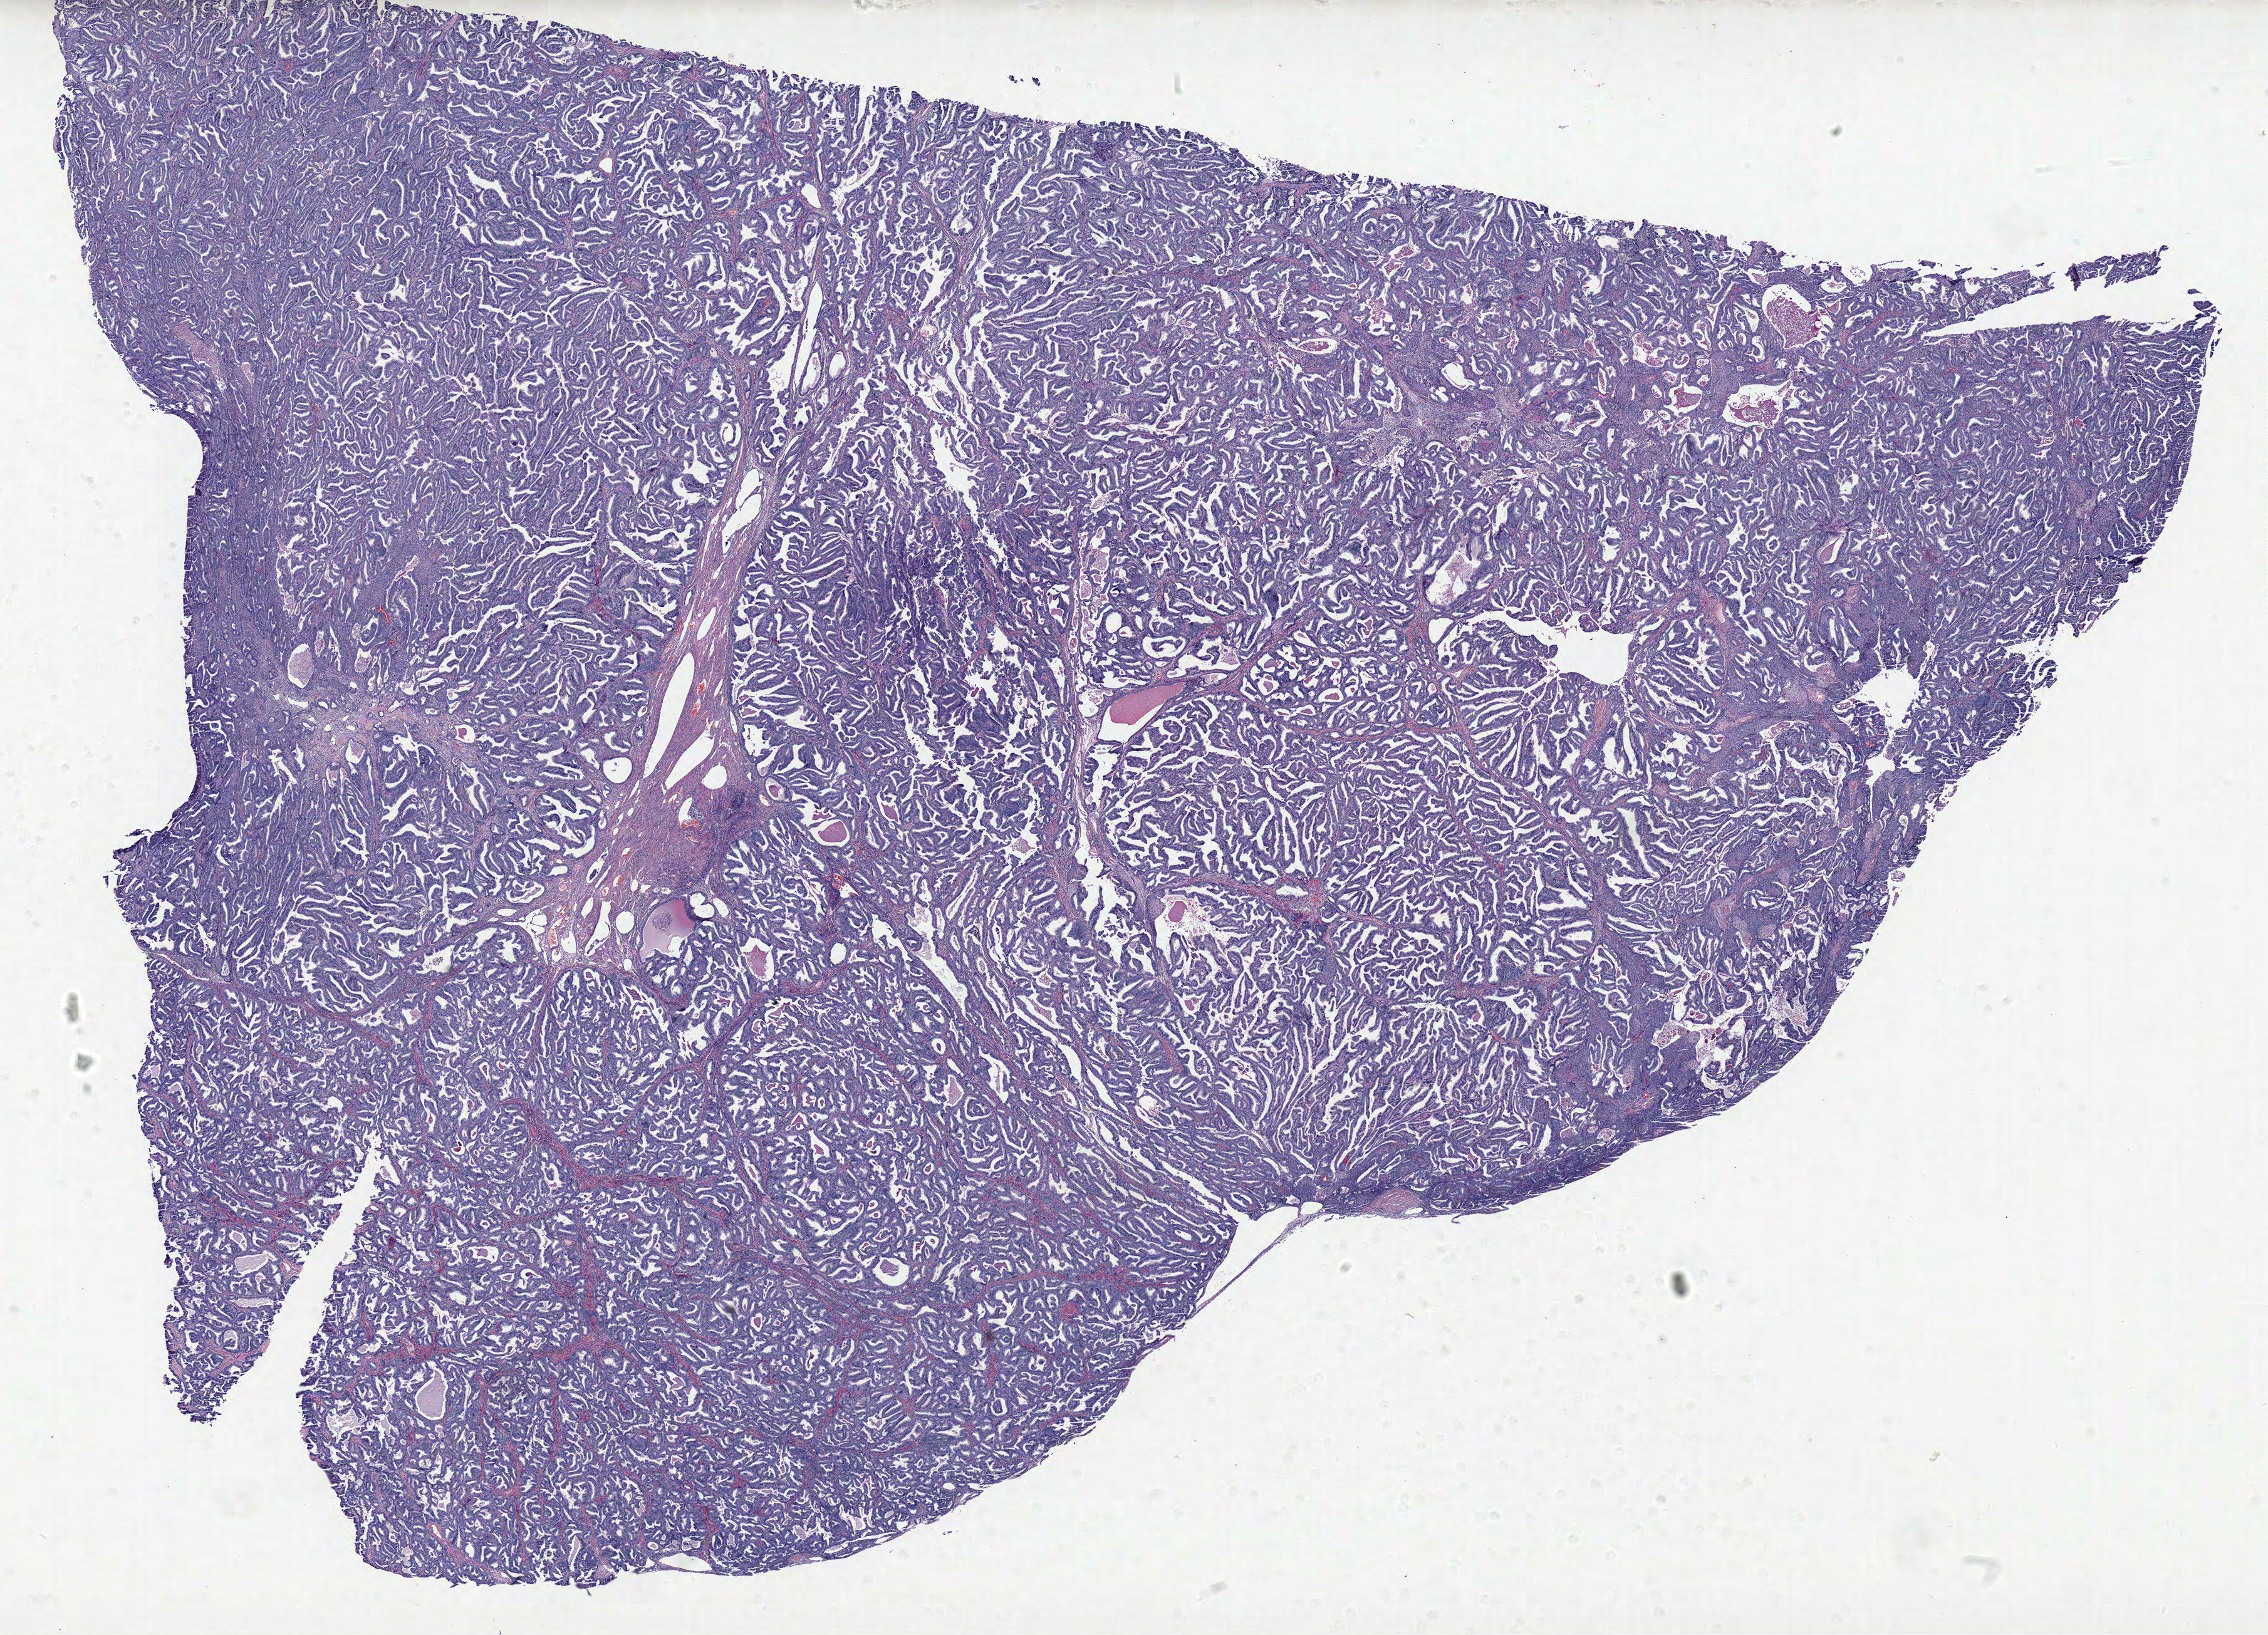
Hematoxylin and eosin (H&E) stained whole-slide image — low-resolution overview of the scanned area, about 28.8 x 20.8 mm; formalin-fixed paraffin-embedded (FFPE) diagnostic section; primary tumour sample from the uterus. Female patient; age at initial diagnosis 56 years. Histologic grade: G1 (well differentiated).
FIGO stage: IA. Histologic diagnosis: Endometrioid adenocarcinoma, NOS (endometrium).